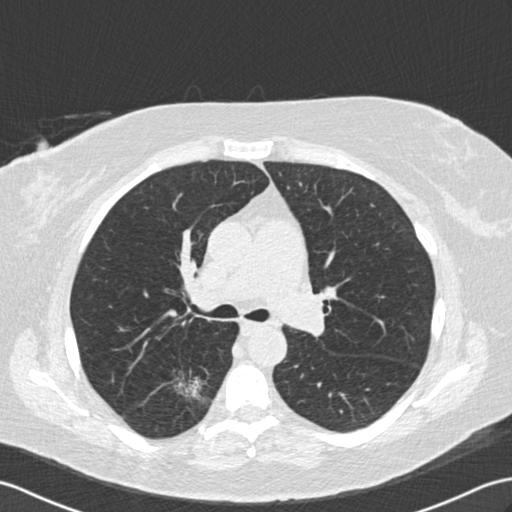
Low-dose screening chest CT, one axial slice. Slice 98 of 154 in the series (ordered by position). Reconstruction kernel B30f. Lung window (W 1500 / L -600 HU). 512 × 512 image matrix, field of view 352 × 352 mm.
Outlined on this slice (expert manual segmentation):
- lesion 1 (tumor, lower lobe of right lung): box from (x=175, y=376) to (x=203, y=400) px